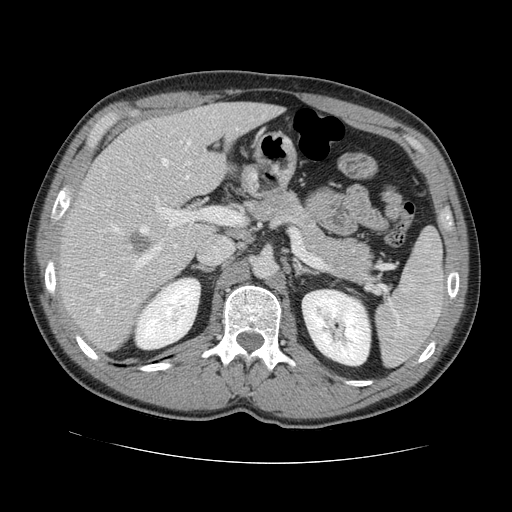
Contrast-enhanced abdominal CT, one axial slice; soft-tissue window (W 400 / L 40 HU); 2.5 mm slice thickness; 512 × 512 image matrix, field of view 380 × 380 mm. Male patient, age 40 years. Case-level facts recorded for this patient, not image findings: diagnosis: colorectal cancer liver metastases, imaged before liver resection.
Annotated regions visible in this slice (manually delineated by an expert):
- hepatic veins: bounding box [x1, y1, x2, y2] px = [96, 139, 191, 313]
- liver: [61, 103, 279, 350]
- planned liver remnant (the part of the liver to remain after resection): [105, 103, 278, 199]
- portal vein (with intrahepatic branches): [101, 196, 234, 292]
- liver metastasis: [130, 232, 156, 256]